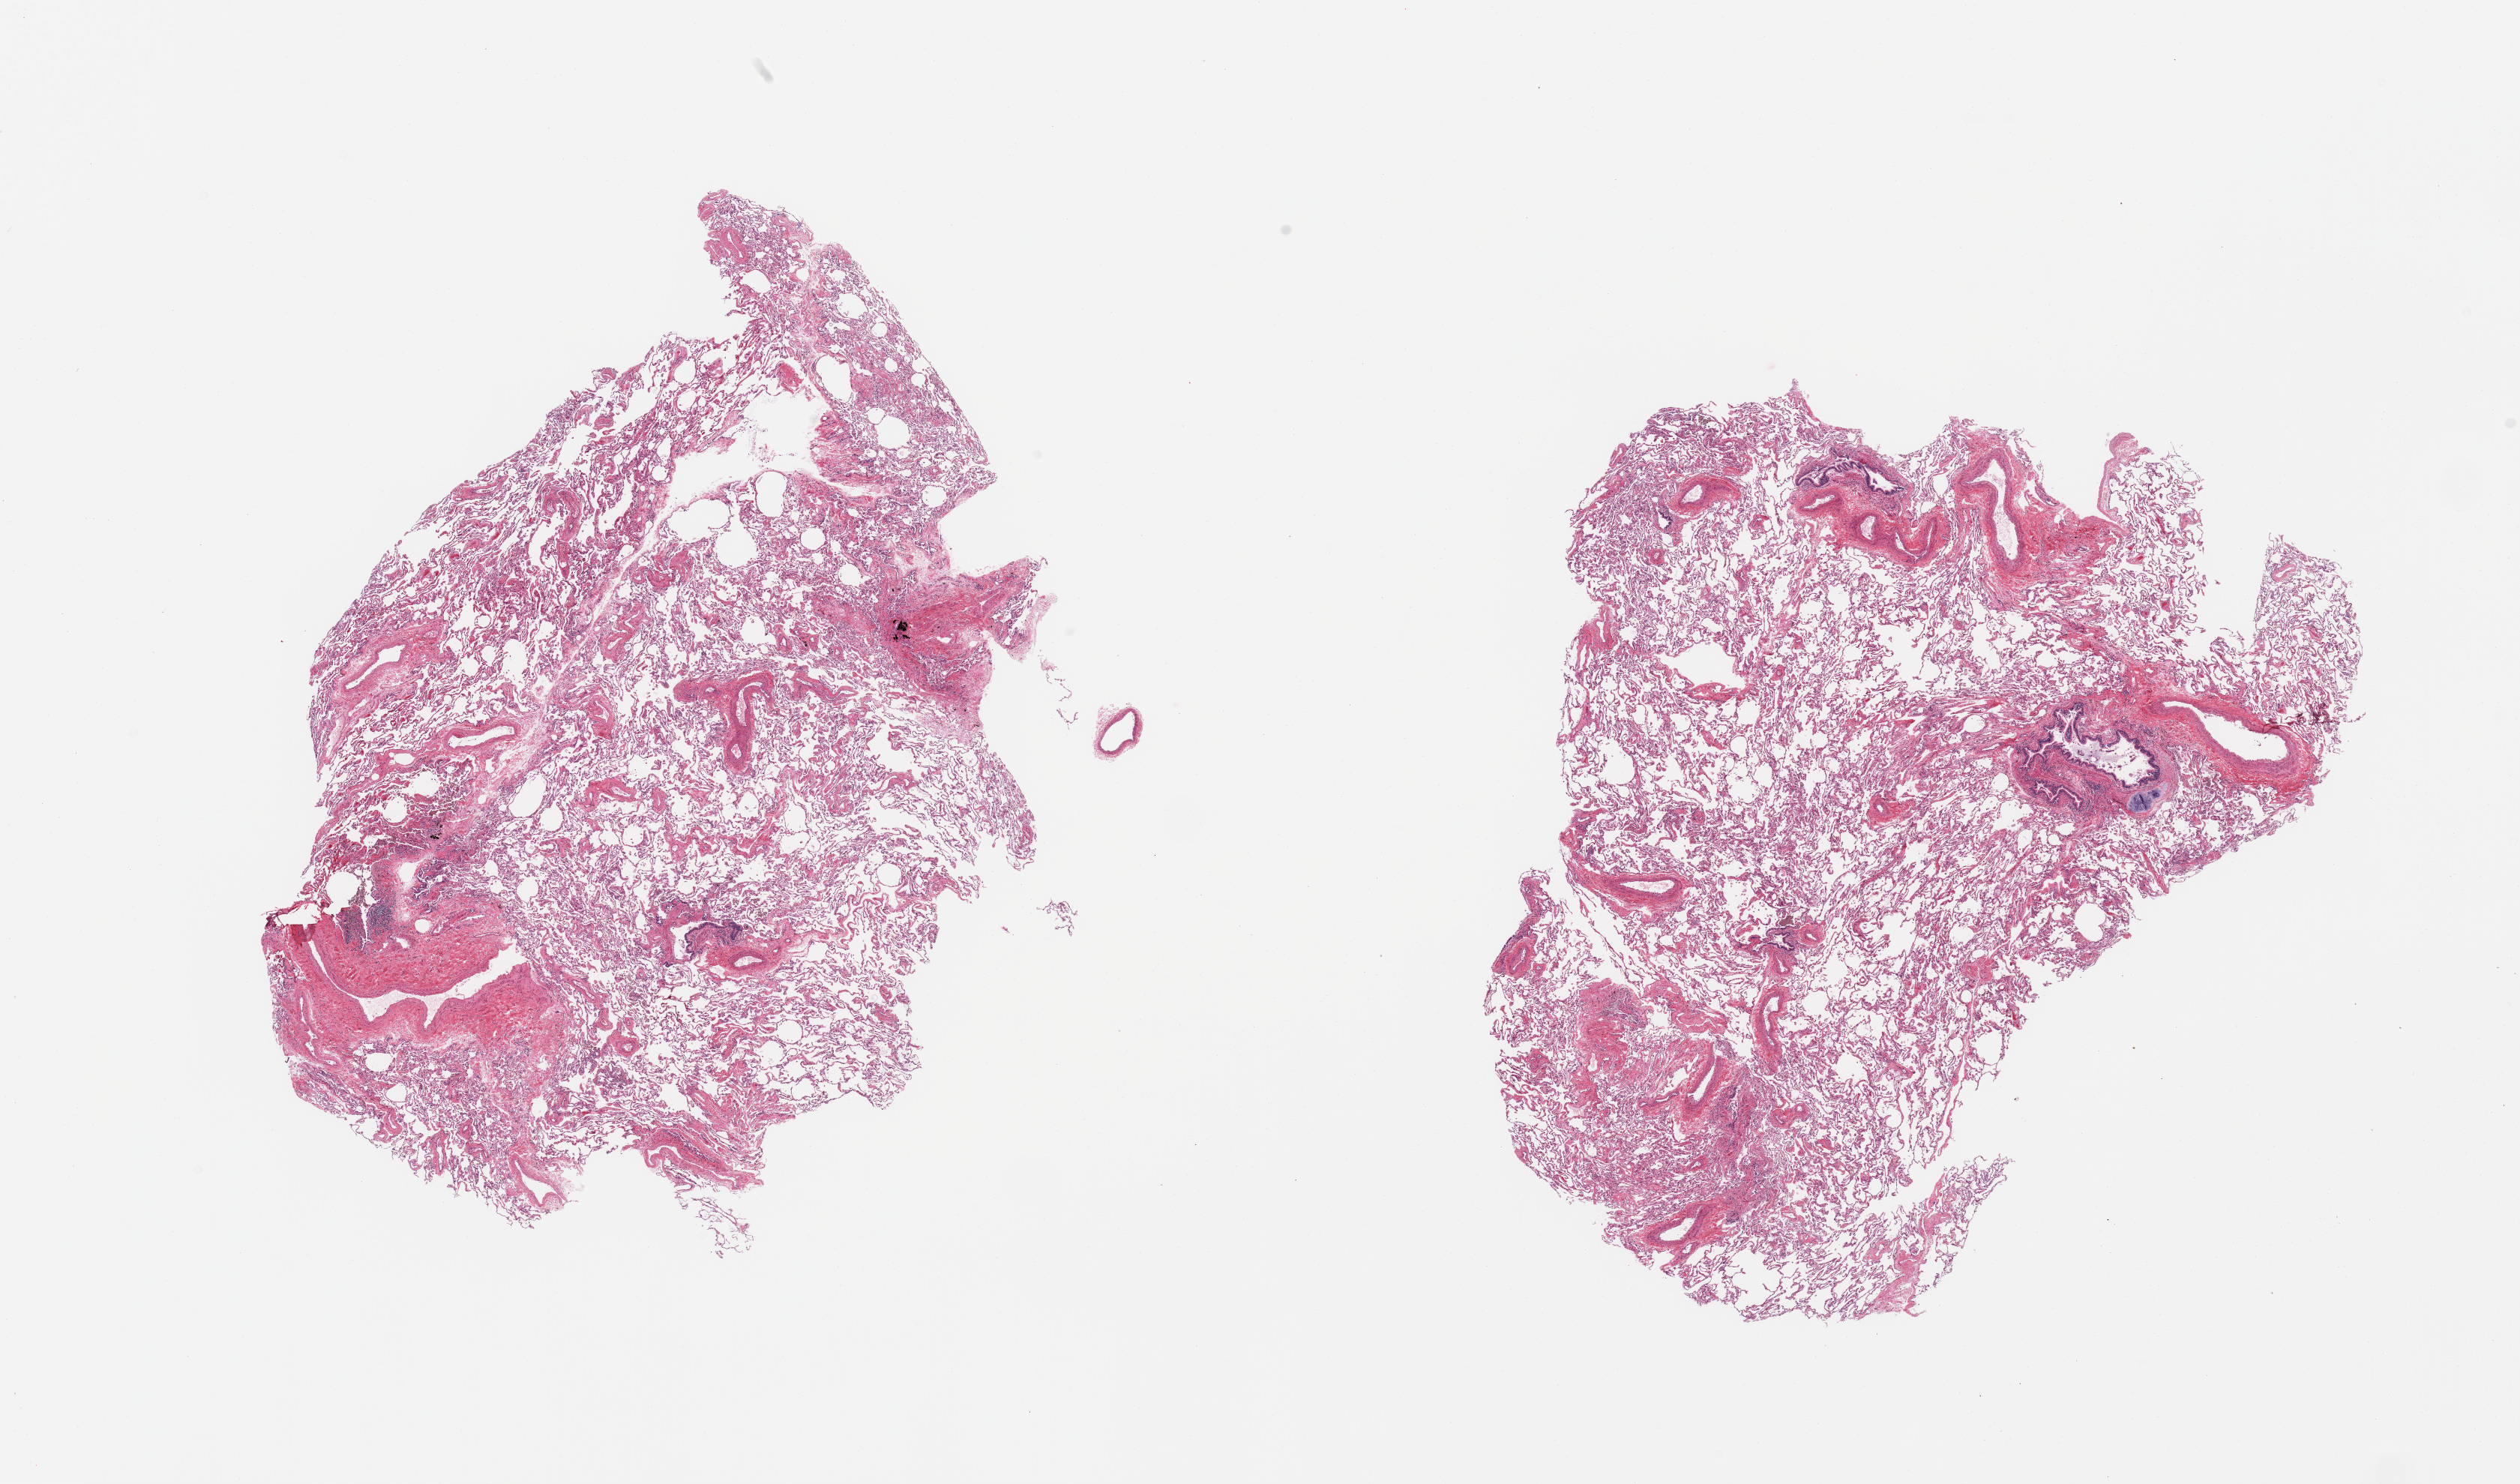
Whole-slide image, H&E stain, brightfield, shown as a low-resolution overview of the whole scanned area (about 26.6 x 15.7 mm). PAXgene-fixed paraffin-embedded (PFPE) section. Sampled site (target tissue): lung. Tissue donor sample.
Pathologist's review note for this sample: 2 pieces, mild congestion.